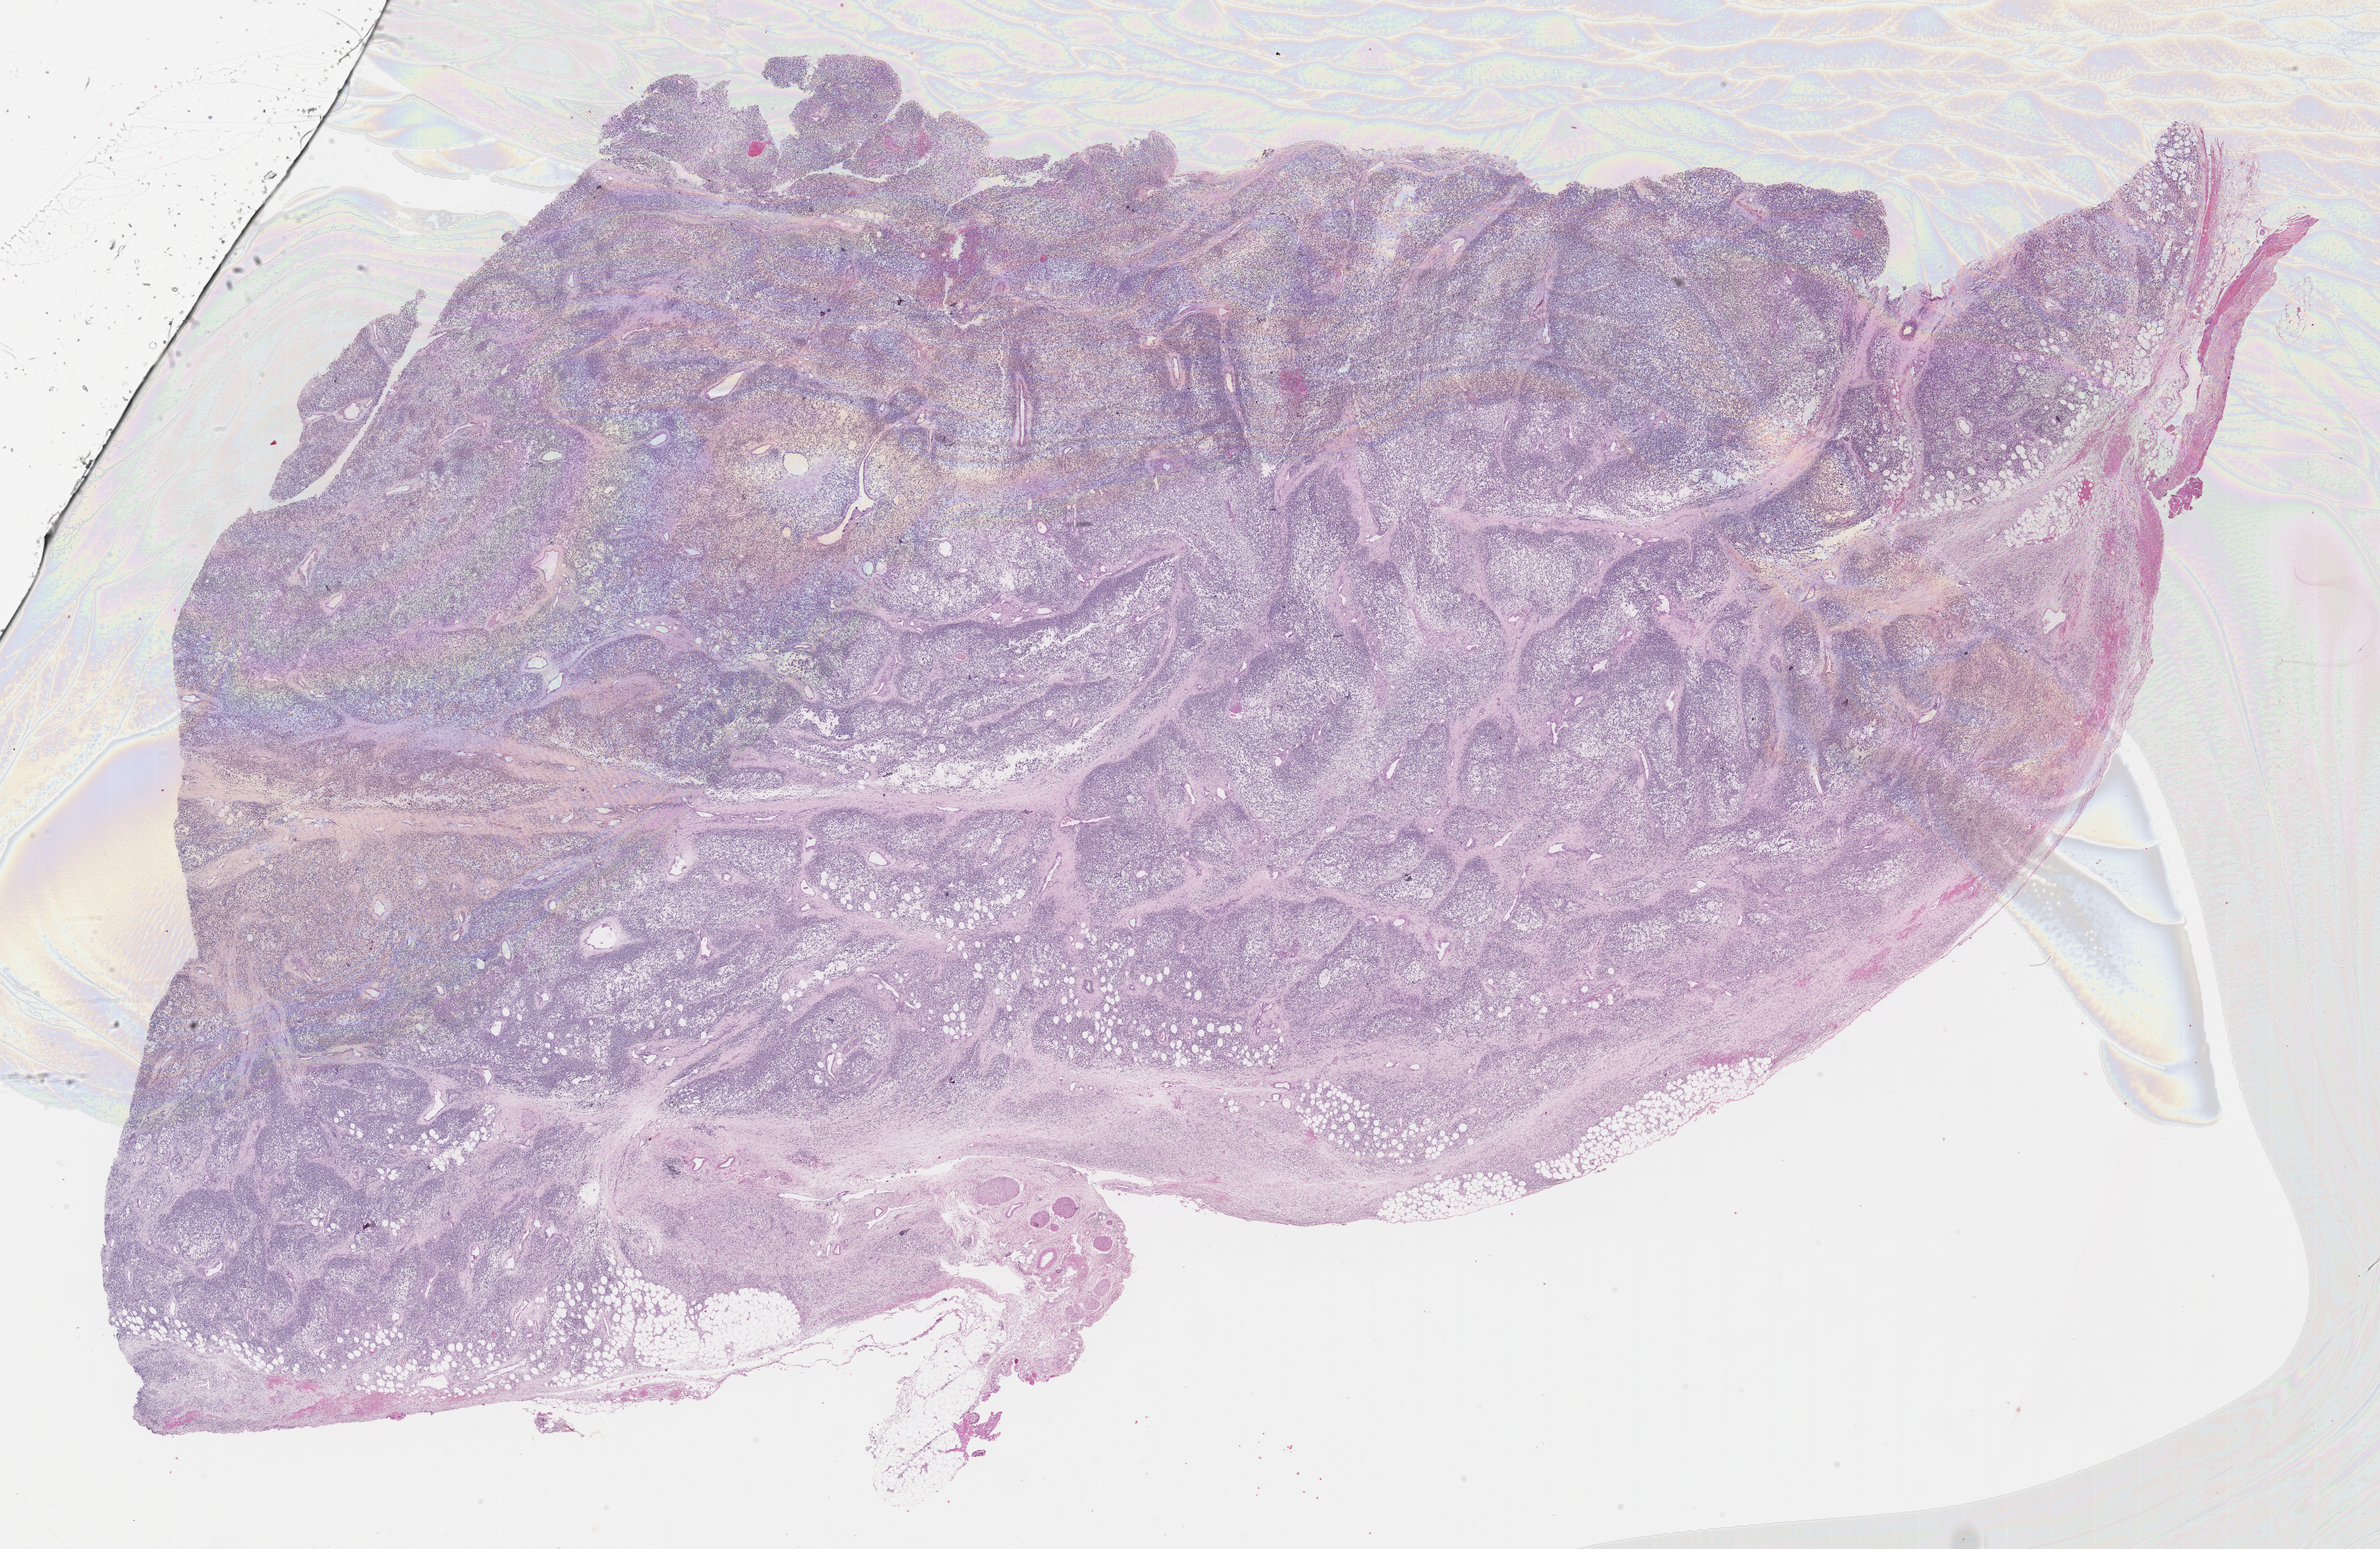
Whole-slide image, H&E stain of tumor tissue — whole scanned area (about 27.2 x 17.7 mm) shown as a low-resolution overview. Formalin-fixed paraffin-embedded section. Sample anatomic site: pelvis. Female patient, age at diagnosis 9.2 years.
Primary site (case record): retroperitoneum. Diagnosis: rhabdomyosarcoma; histological classification: embryonal rhabdomyosarcoma. Metastatic status at presentation (as recorded): non-metastatic. Stage (as recorded): 3.